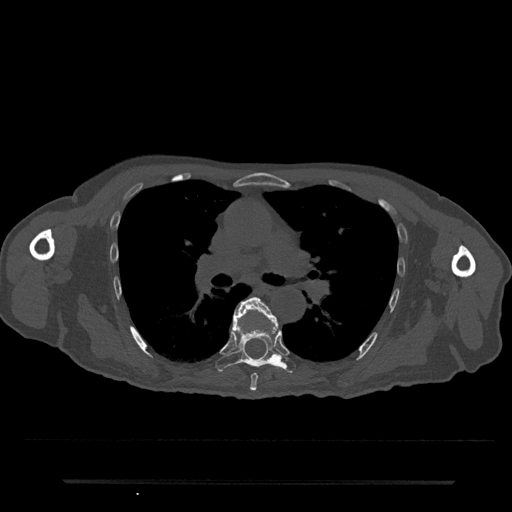
CT including the spine, one axial slice. Position 498 of 797 along the scan axis. Reconstruction kernel Br40s/3. 120 kVp. Bone window (W 1800 / L 400 HU). 0.5 mm slice thickness. 512 × 512 image matrix. Male patient, age 74 years. From the clinical record (not read from this slice): primary cancer: prostate.
Annotated regions visible in this slice (semi-automatically segmented with operator editing):
- T6 vertebra: bounding box (x1, y1, x2, y2) in pixels: (233, 297, 278, 391)
- T7 vertebra: (215, 322, 296, 373)